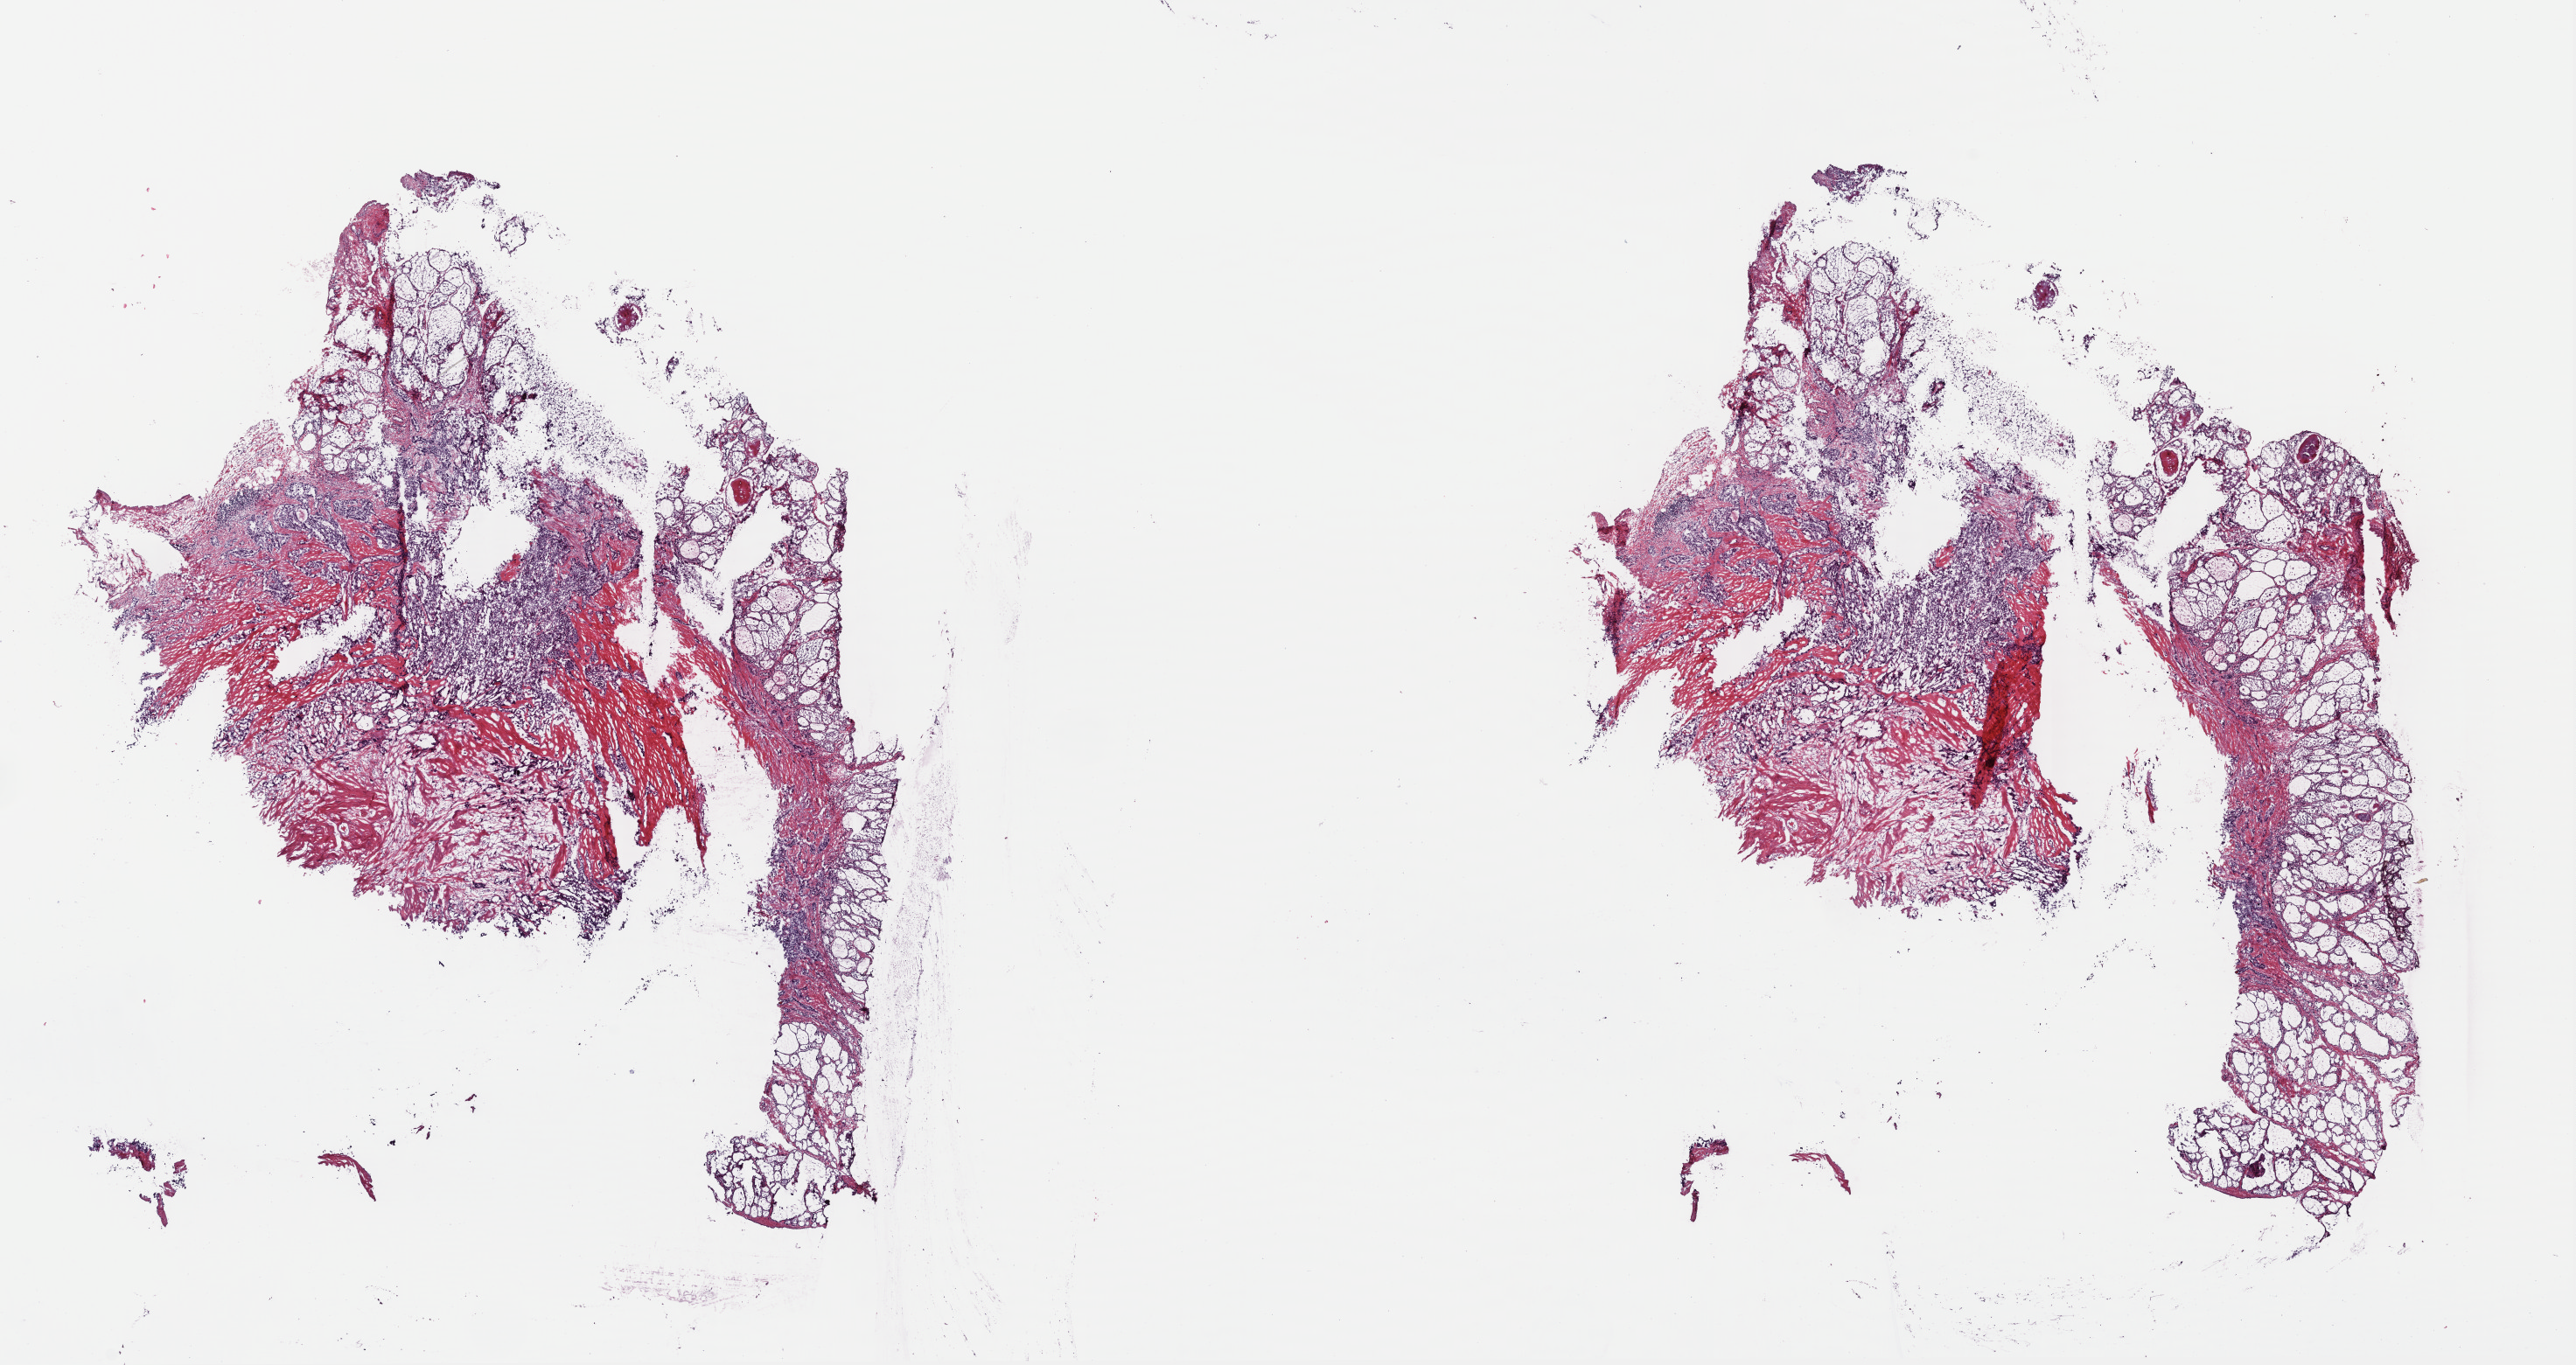
Digitized H&E tissue section (whole slide) — low-resolution overview of the scanned area, about 23.1 x 12.3 mm (slide scanned at 40x); frozen section from the top of the tissue portion; primary tumour sample from the thyroid. Patient: female, age at initial diagnosis 48 years. Pathologist review of this section (percent, as recorded): tumour cells 75%, tumour nuclei 75%, normal cells 0%, stromal cells 25%, necrosis 0%. Infiltration values recorded for this section: lymphocyte infiltration 5%, monocyte infiltration 0%, neutrophil infiltration 0%.
Diagnosis: Papillary carcinoma, columnar cell (thyroid gland). TNM: T1a N0 M0. Laterality: bilateral. AJCC pathologic stage: I (7th edition).